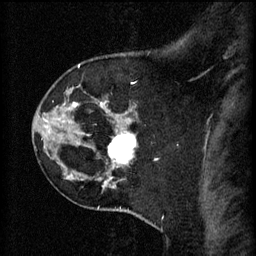
Breast MRI (dynamic contrast-enhanced), one sagittal slice. Position 47 of 60 along the scan axis. 3 images stored at this slice position (order not interpretable as contrast timing). 1.5 T. TE 4.2 ms, TR 11 ms. 2 mm slice thickness. 256 × 256 image matrix, field of view 180 × 180 mm. Female patient, age 45 years.
Outlined on this slice (semi-automatically segmented with operator editing):
- analysis volume of interest (the breast-tissue region the enhancement analysis was run in; not a lesion): box from (x=108, y=128) to (x=137, y=171) px
- tumour enhancement mask (voxels above the 70 % enhancement threshold inside the analysis volume of interest): (x=110, y=132)–(x=137, y=165)